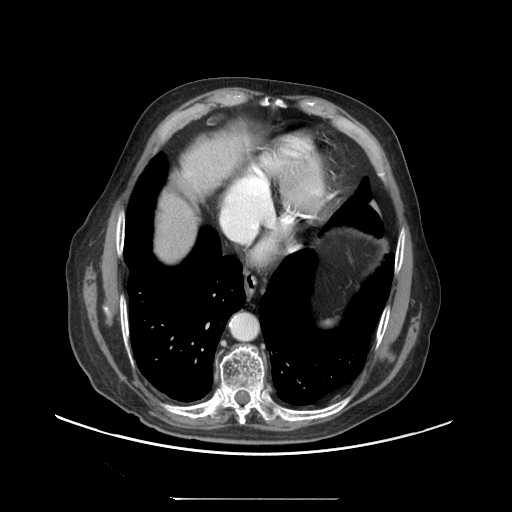
Contrast-enhanced abdominal CT (liver protocol), one axial slice. Position 87 of 97 along the scan axis. Soft-tissue window (W 400 / L 40 HU). 2.5 mm slice thickness. 512 × 512 image matrix. From the clinical record (not read from this slice): diagnosis: hepatocellular carcinoma (patient treated with transarterial chemoembolisation; whether this scan precedes or follows treatment is not stated here); TNM stage (as recorded): Stage-IIIC; Child-Pugh class: A; tumour differentiation: well differentiated; tumour size: 9.2 cm.
Annotated regions visible in this slice (semi-automatic segmentation, software-assisted and operator-edited):
- abdominal aorta: bounding box (x1, y1, x2, y2) in pixels: (231, 313, 257, 340)
- liver parenchyma outside the tumour (the mass and vessels are separate outlines, so this box may not span the whole liver): (156, 170, 213, 260)